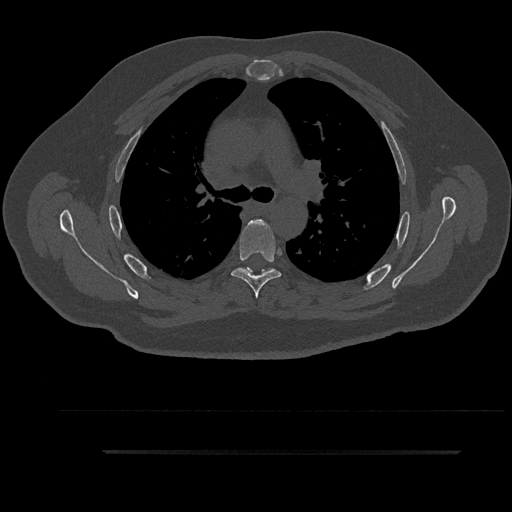
CT including the spine, one axial slice. Slice 626 of 797 in the series (ordered by position). Reconstruction kernel Br40s/3. Bone window (W 1800 / L 400 HU). 512 × 512 image matrix, field of view 432 × 432 mm. Male patient, age 63 years. Case-level facts recorded for this patient, not image findings: primary cancer: renal.
Annotated regions visible in this slice (semi-automatically segmented with operator editing):
- T4 vertebra: box from (x=248, y=219) to (x=260, y=225) px
- T5 vertebra: (x=231, y=219)–(x=281, y=299)
- T6 vertebra: (x=243, y=268)–(x=274, y=276)